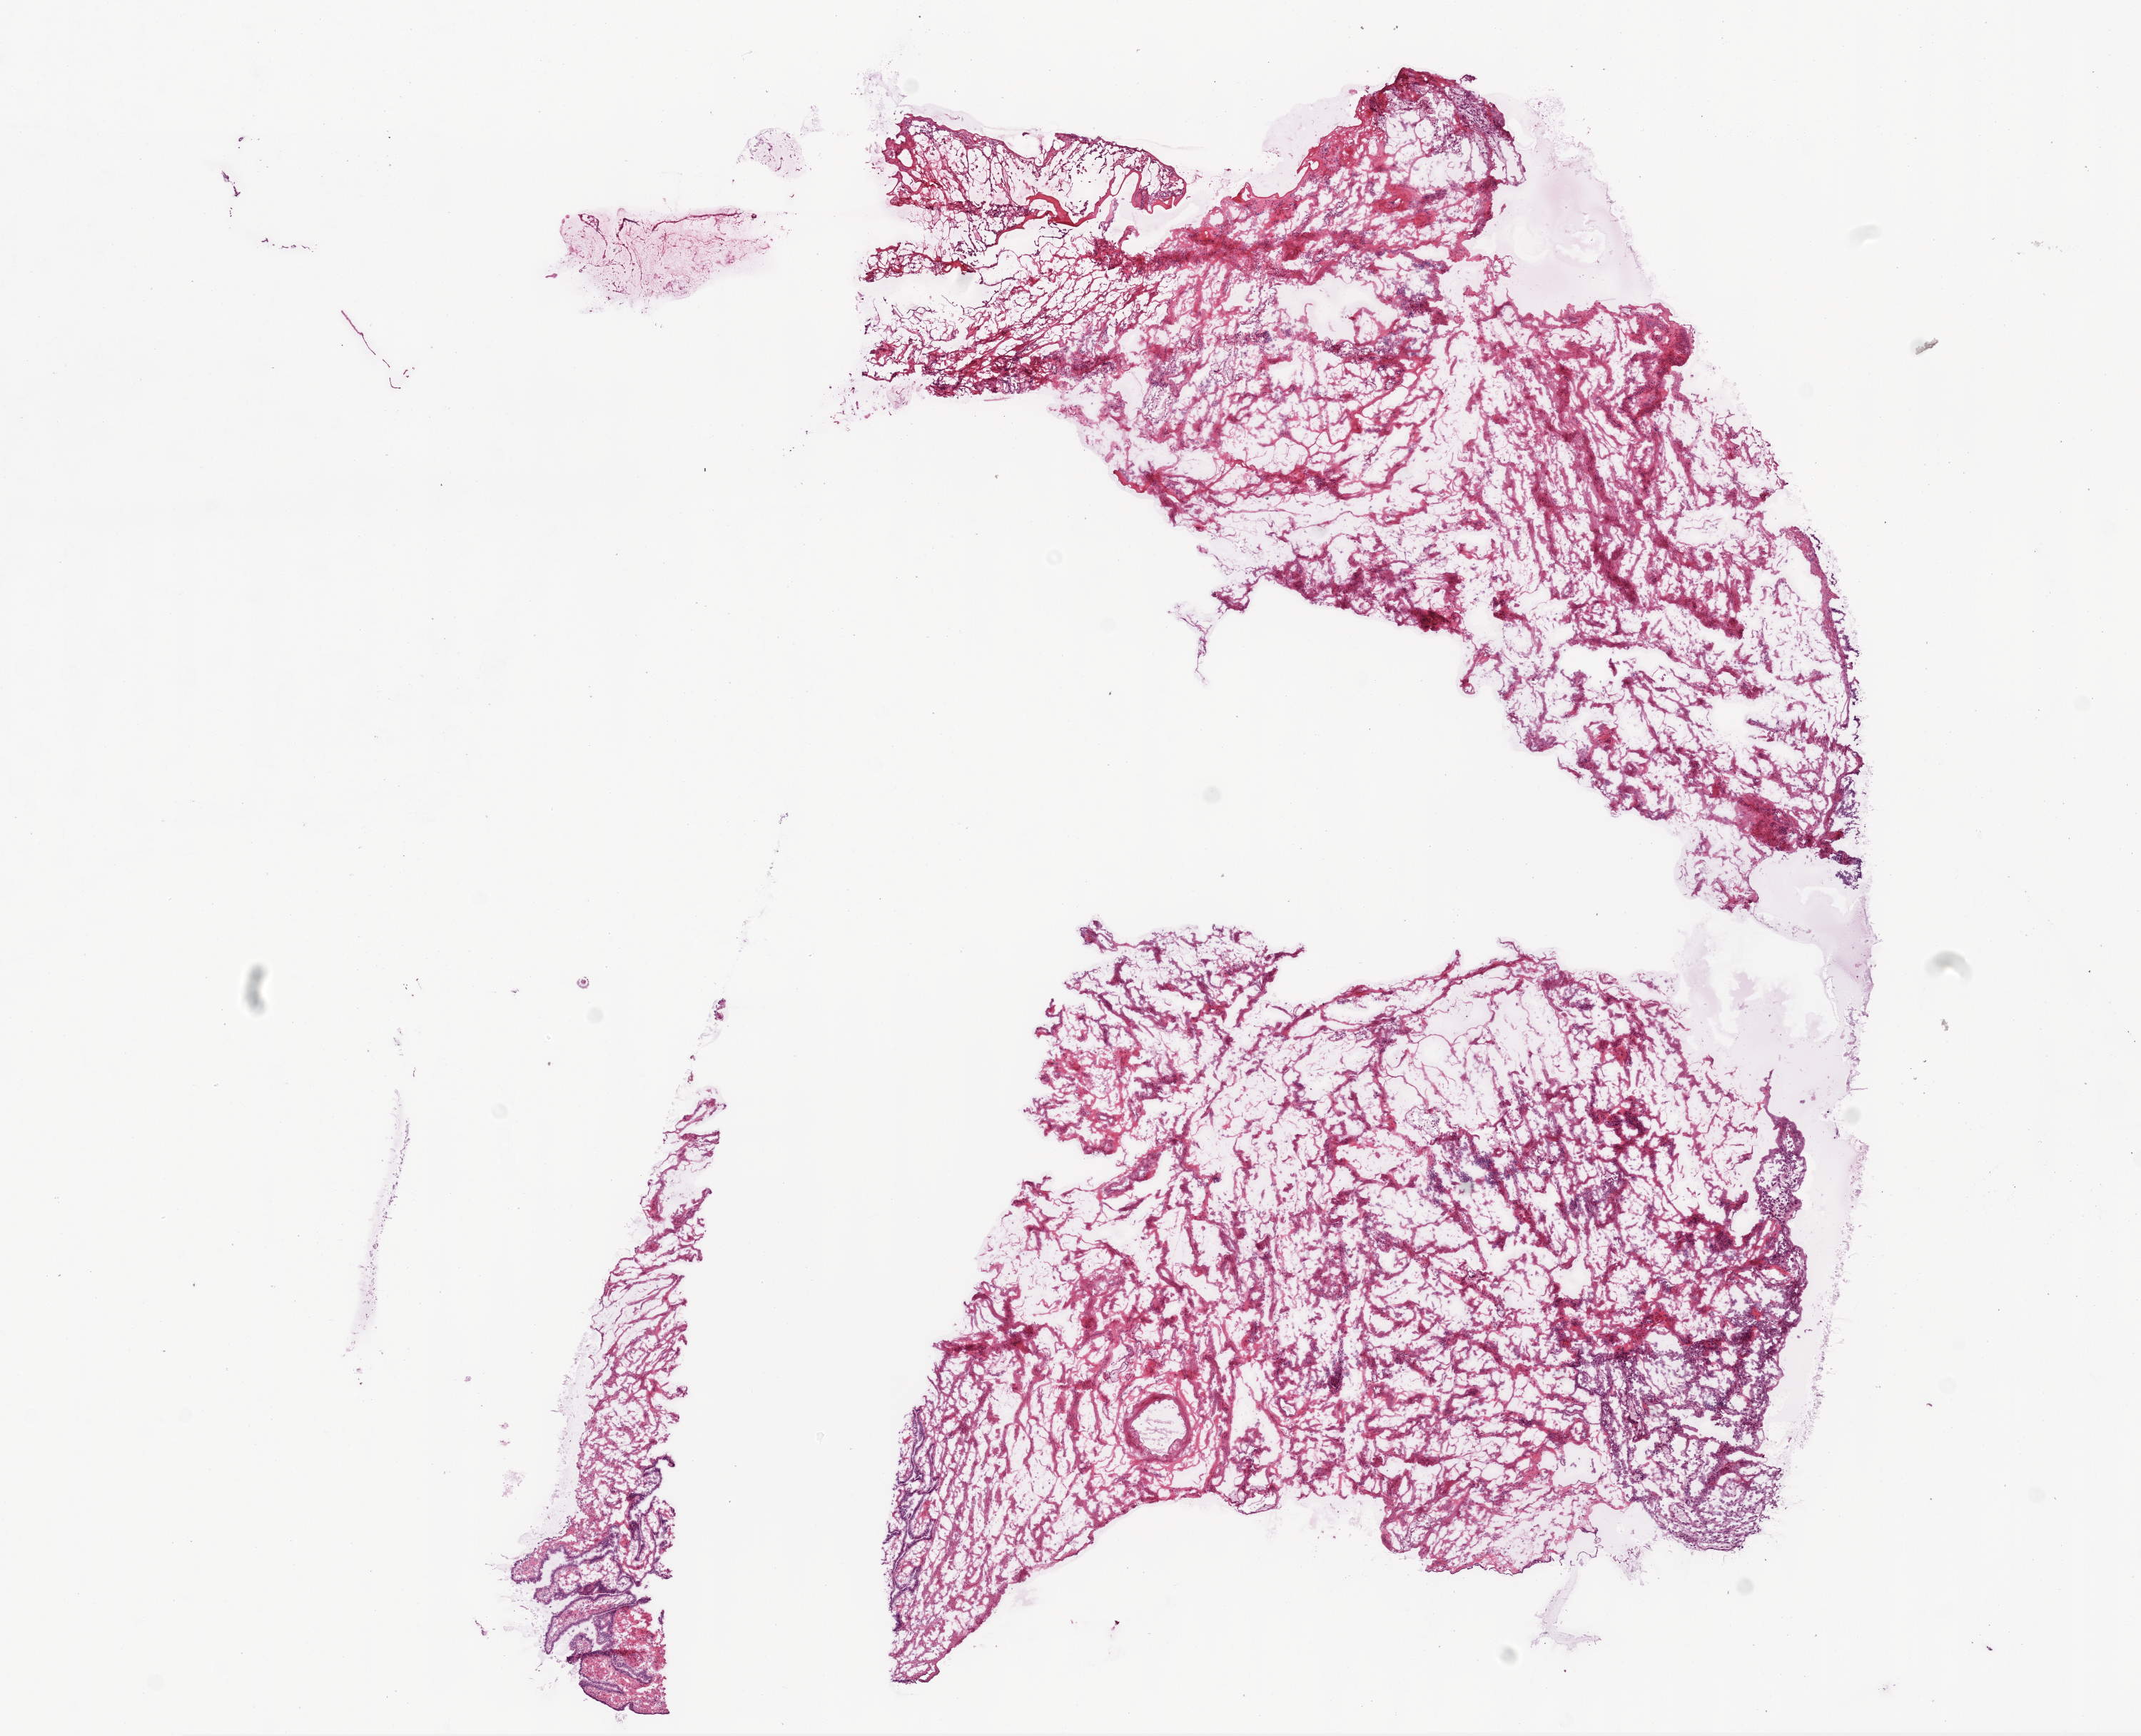
Whole-slide histology image, Hematoxylin and eosin (H&E) stained, shown as a low-resolution overview of the whole scanned area (about 12.0 x 9.8 mm, from a 20x scan). Frozen section from the bottom of the tissue portion. Ovary, solid tissue normal (non-tumour tissue) sample. Patient: female, age at initial diagnosis 46 years.
This section: solid tissue normal (non-tumour) sample from the same patient. Patient diagnosis: Serous cystadenocarcinoma, NOS.